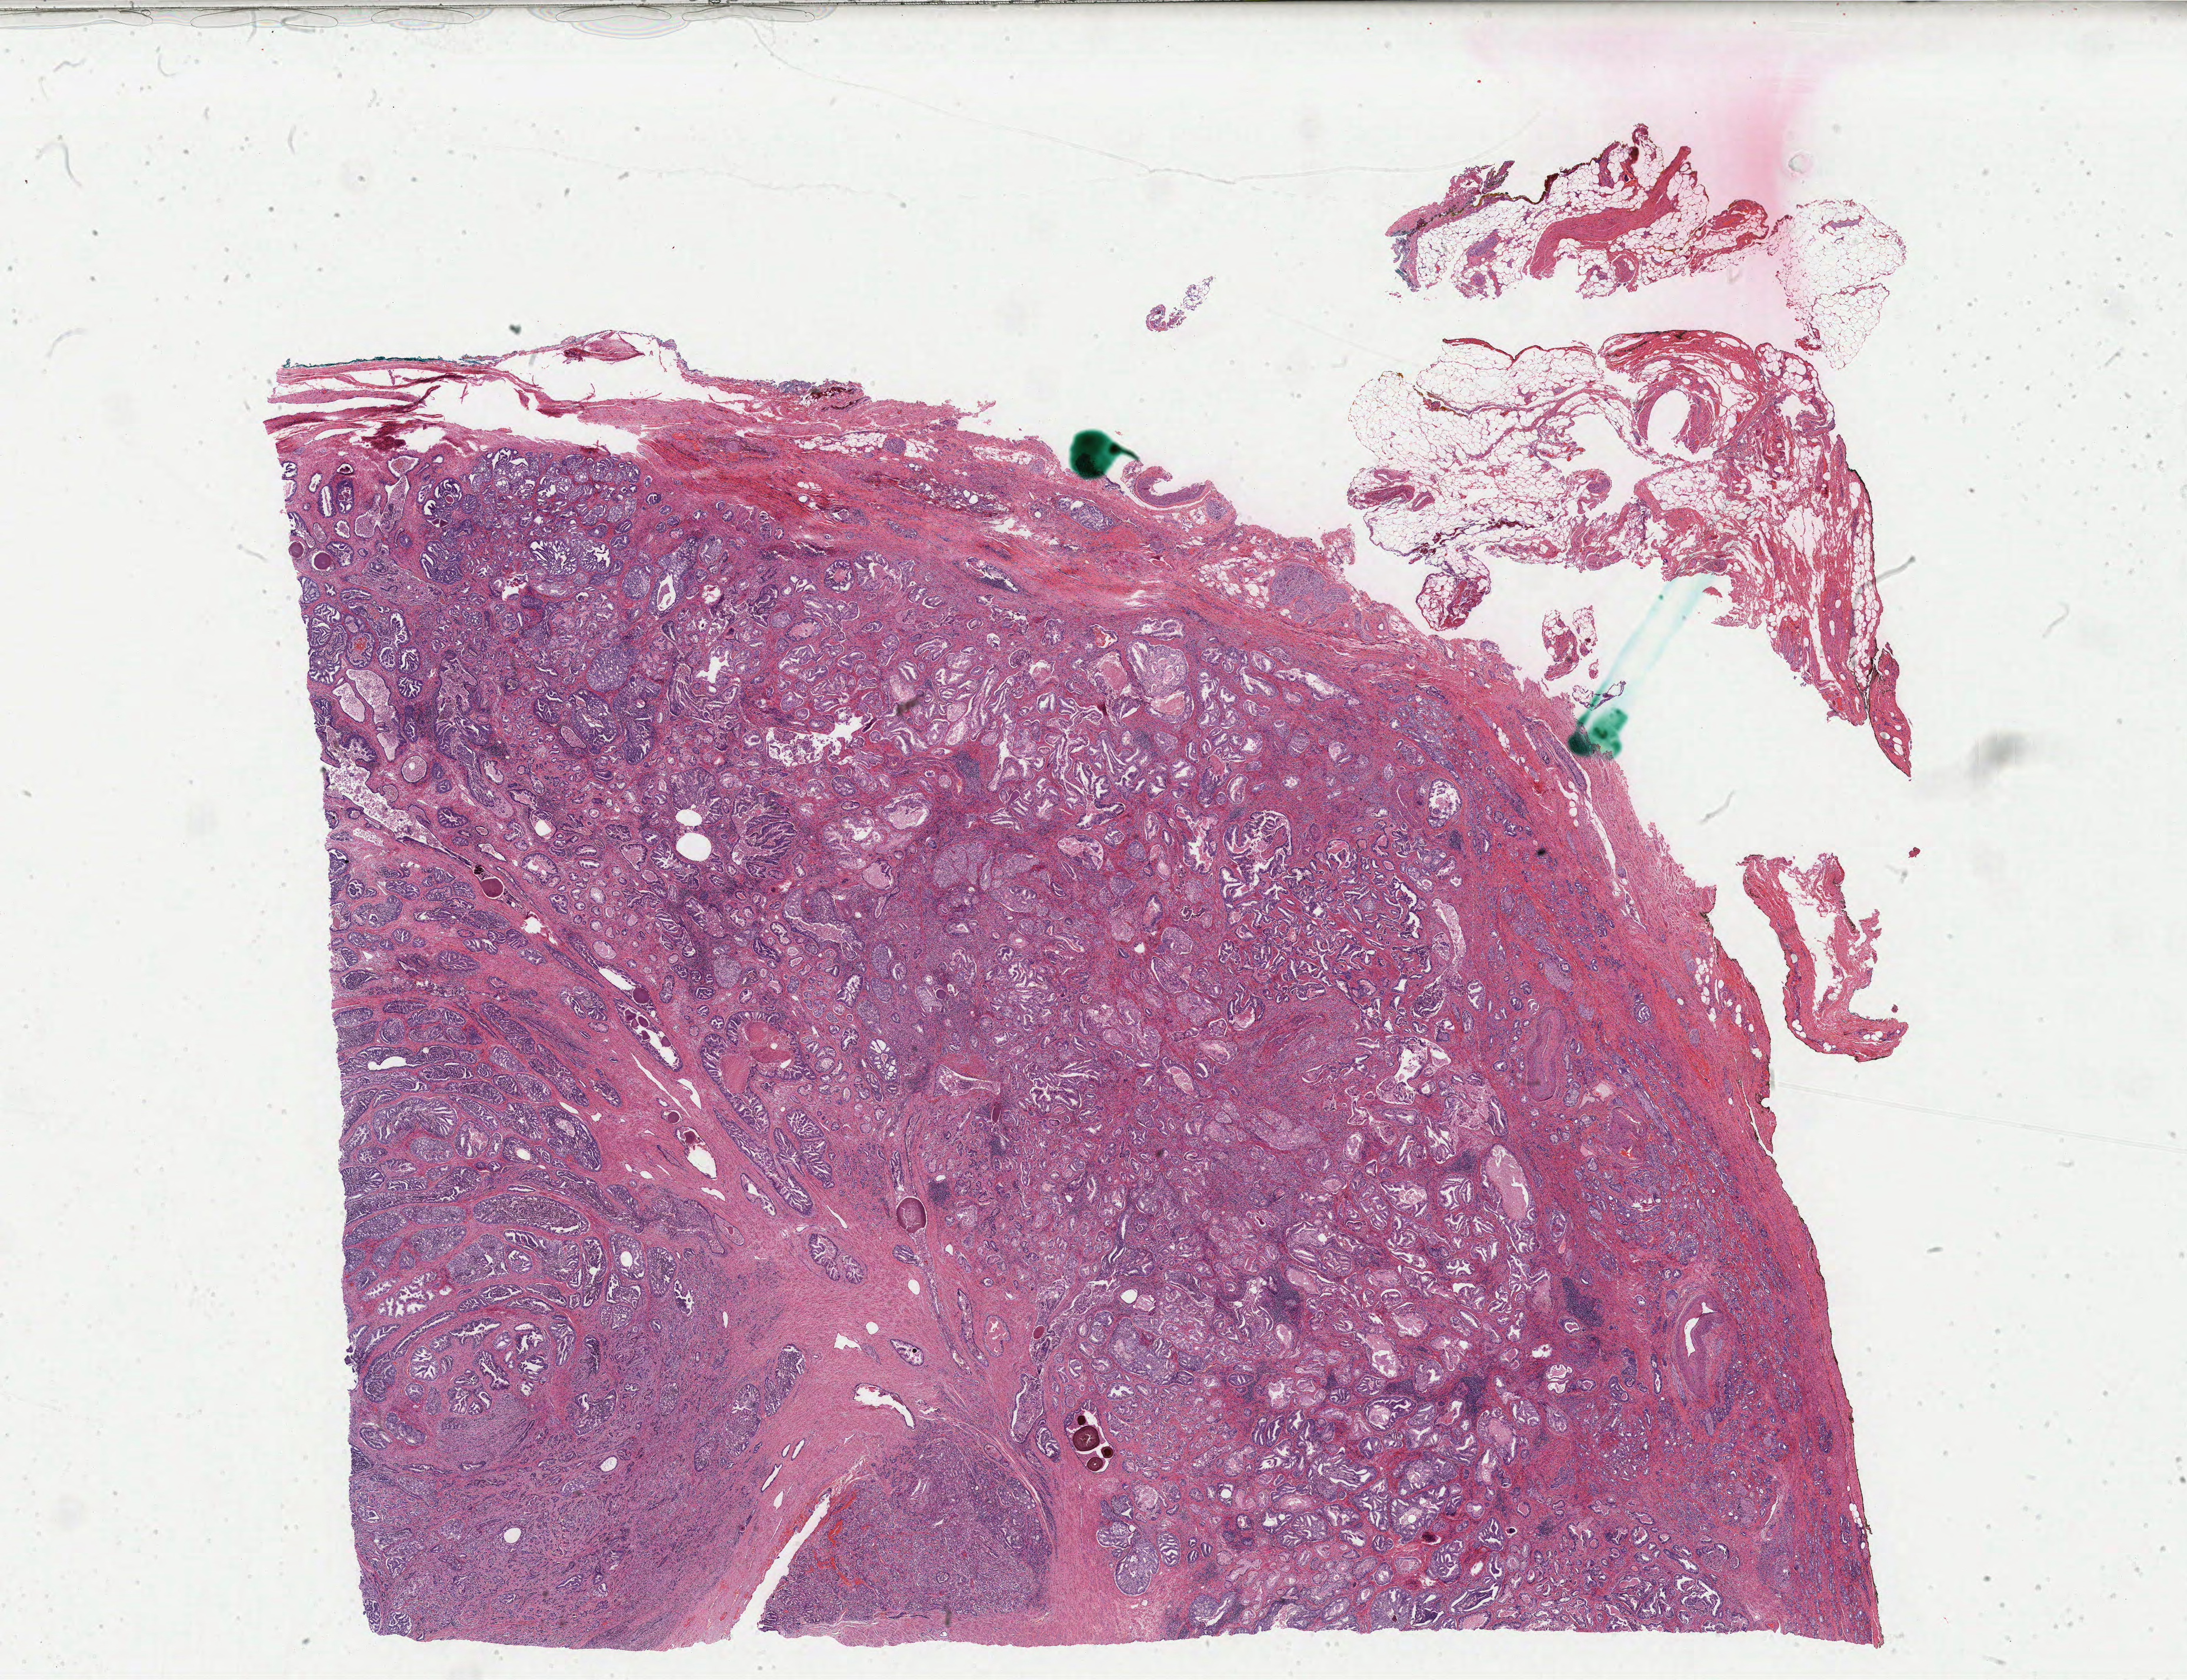
Hematoxylin and eosin (H&E) stained whole-slide image — whole scanned area (about 29.5 x 22.7 mm, from a 40x scan) shown as a low-resolution overview; formalin-fixed paraffin-embedded (FFPE) diagnostic section; primary tumour sample from the prostate. Patient: male, age at initial diagnosis 69 years. Gleason score: 9 (4+5).
Pathologic diagnosis: Adenocarcinoma, NOS (prostate gland). Lymph nodes positive (case pathology): 3 of 19 examined.